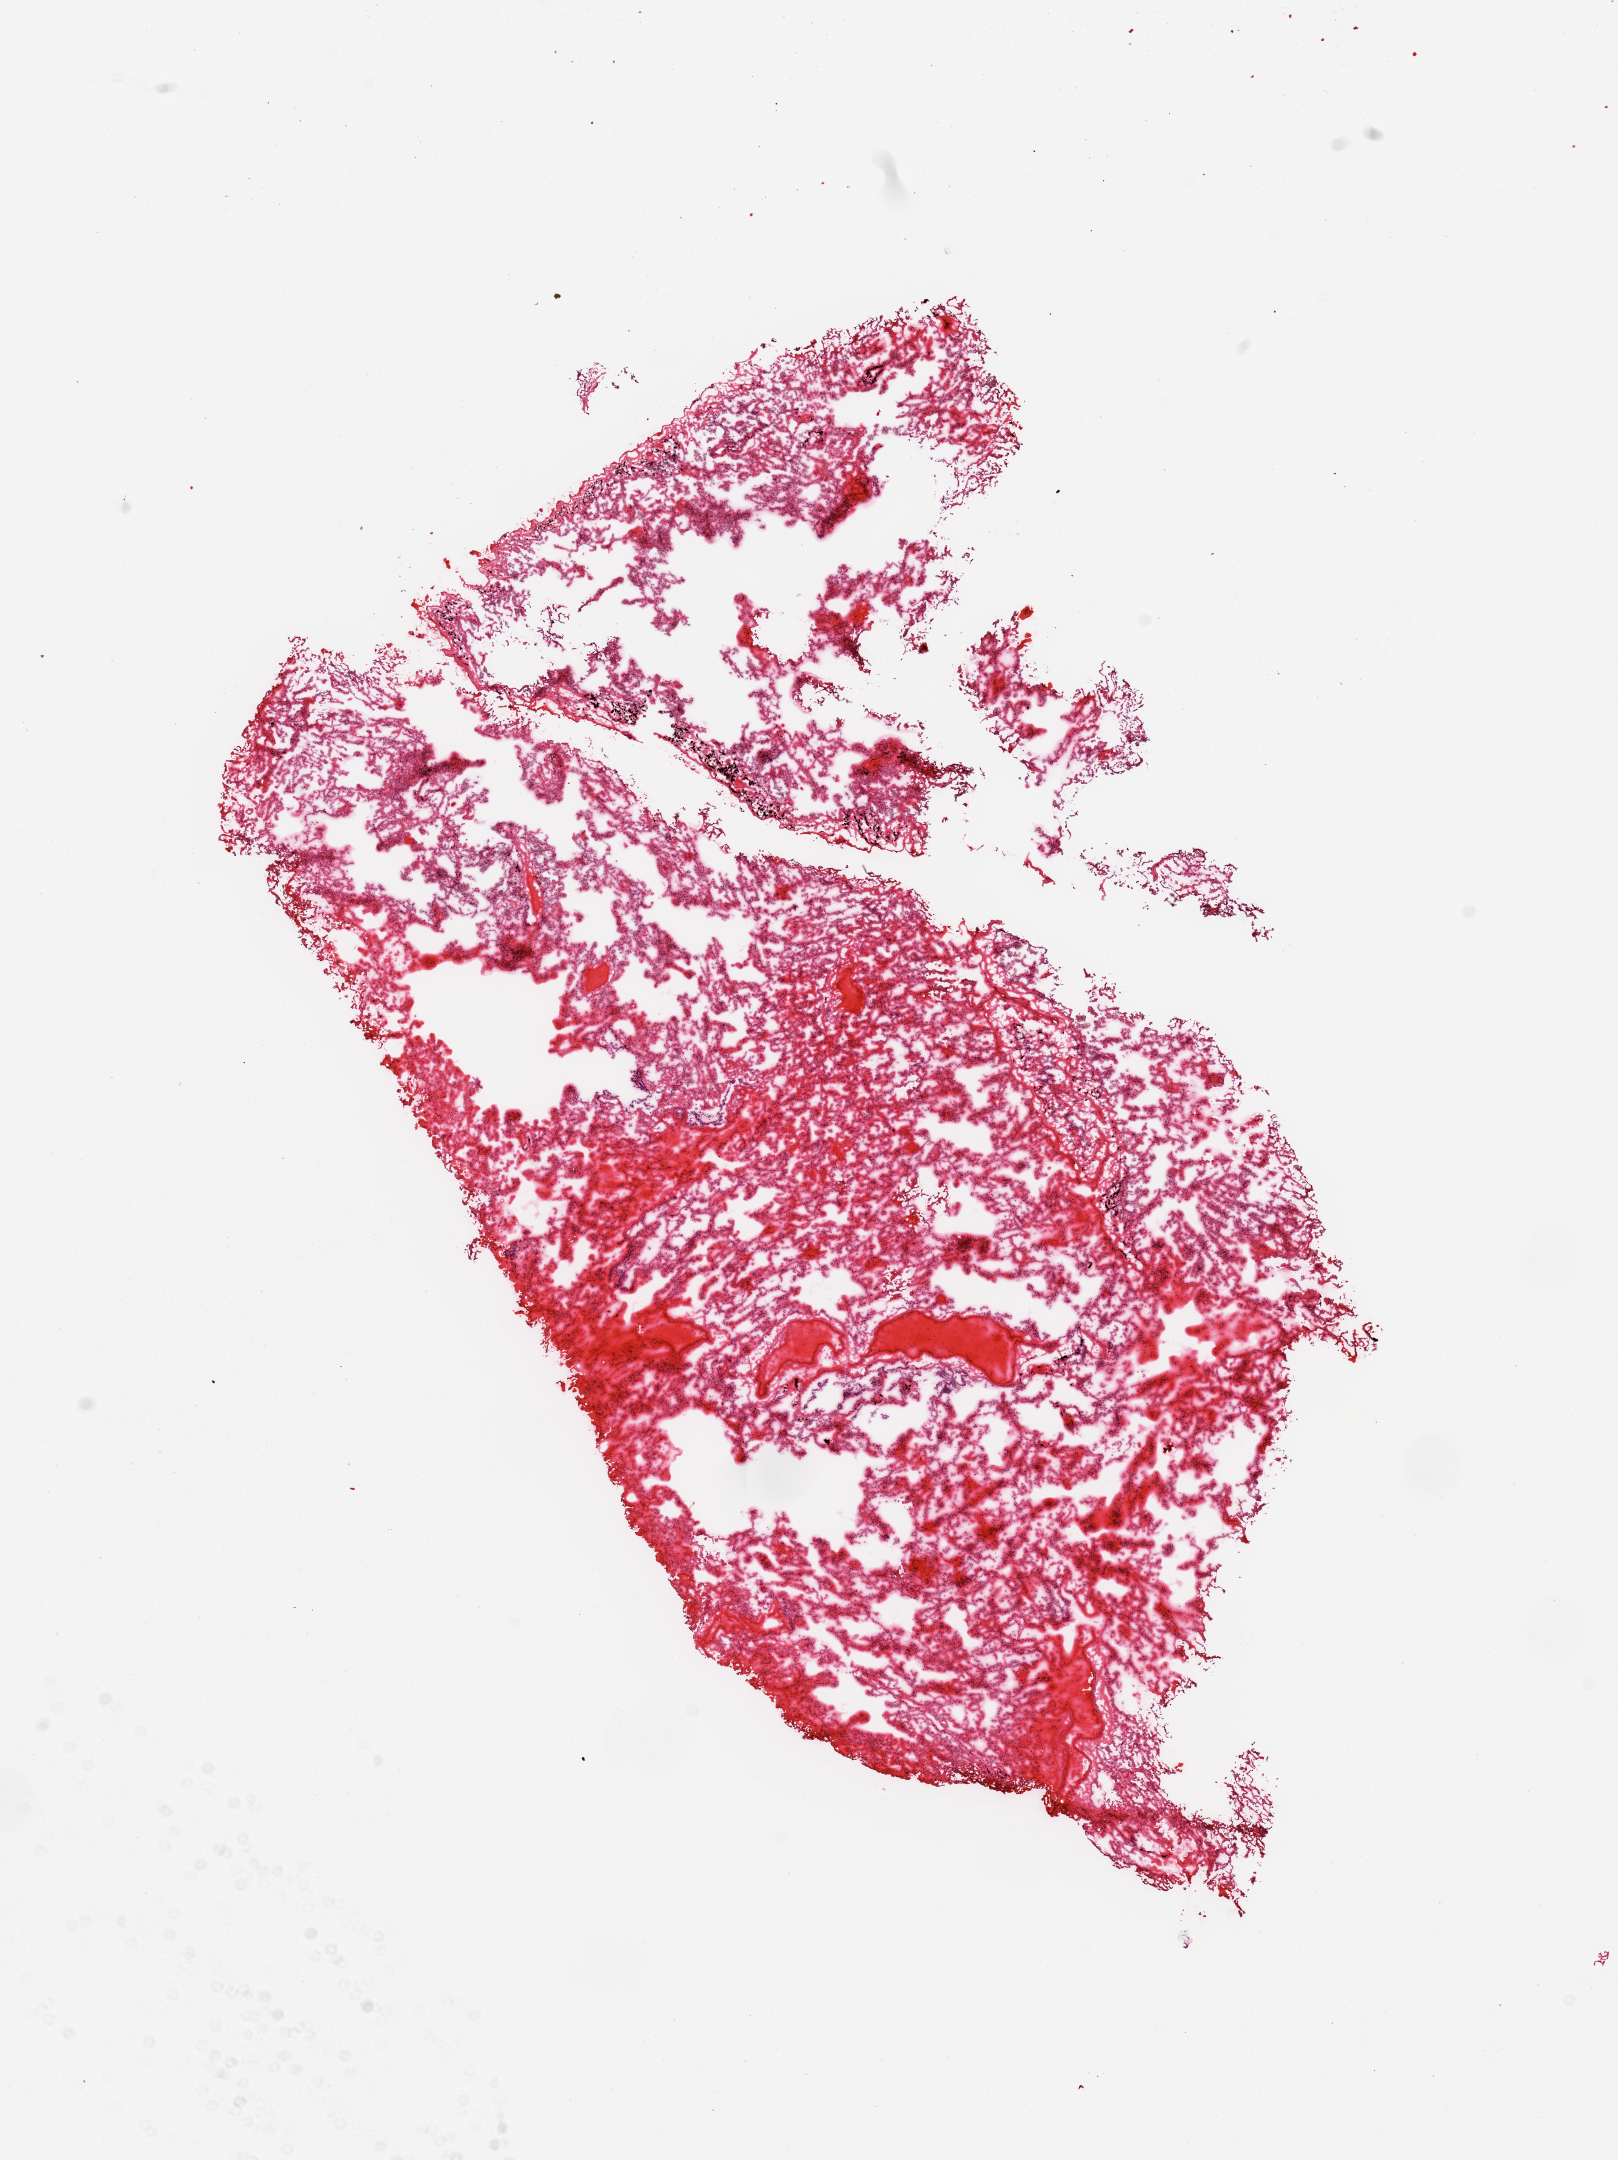
Whole-slide image, H&E stain, shown as a low-resolution overview of the whole scanned area (about 12.8 x 17.1 mm), frozen section, sampled site (target tissue): lung, donor tissue sample. Donor: male.
Review note (as recorded): 1 piece.